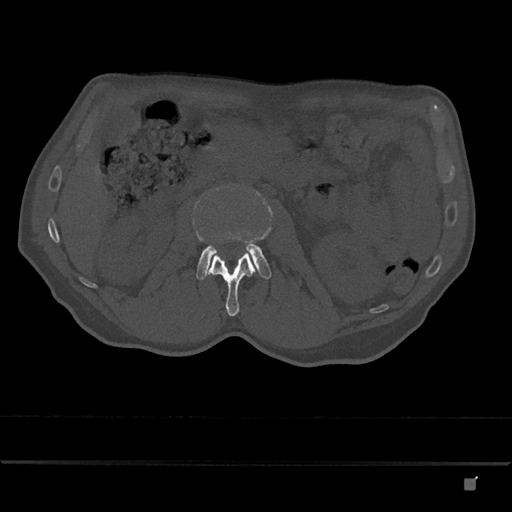
CT including the spine, one axial slice. Slice 446 of 797 in the series (ordered by position). Reconstruction kernel Br40s/3. 120 kVp. Bone window (W 1800 / L 400 HU). 512 × 512 image matrix. Male patient, age 72 years. From the clinical record (not read from this slice): primary cancer: prostate.
Outlined on this slice (semi-automatically segmented with operator editing):
- L2 vertebra: bounding box [x1, y1, x2, y2] px = [206, 252, 256, 316]
- L3 vertebra: [196, 243, 272, 280]